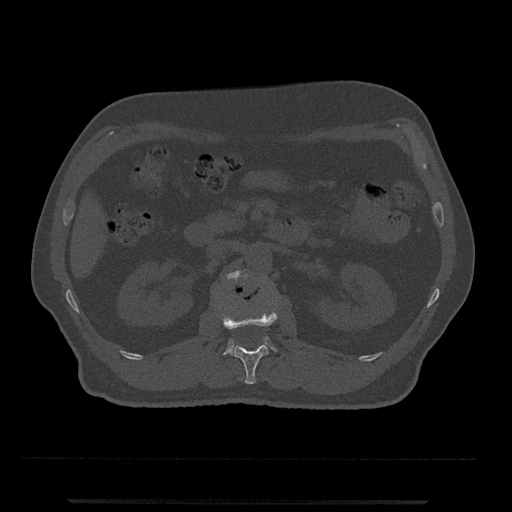
CT including the spine, one axial slice; reconstruction kernel Br40s/3; bone window (W 1800 / L 400 HU); 0.5 mm slice thickness; 512 × 512 image matrix. Male patient, age 63 years. From the clinical record (not read from this slice): primary cancer: prostate.
Outlined on this slice (semi-automatic segmentation, software-assisted and operator-edited):
- L1 vertebra: bounding box (x1, y1, x2, y2) in pixels: (222, 300, 278, 384)
- L2 vertebra: (223, 270, 277, 355)